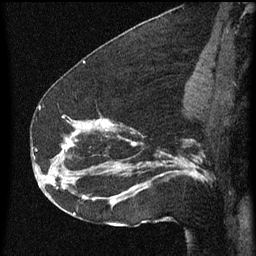
Breast MRI (dynamic contrast-enhanced), one sagittal slice. Position 34 of 60 along the scan axis. Dynamic contrast-enhanced series, image 2 of 3 at this slice position (ordered by acquisition). 1.5 T. TE 4.2 ms, TR 8 ms. 2 mm slice thickness. 256 × 256 image matrix. Patient: female, 52 years.
Structures marked on this image (semi-automatically segmented with operator editing):
- analysis volume of interest (the breast-tissue region the enhancement analysis was run in; not a lesion): box from (x=54, y=116) to (x=178, y=207) px
- tumour enhancement mask (voxels above the 70 % enhancement threshold inside the analysis volume of interest): (x=61, y=116)–(x=178, y=203)